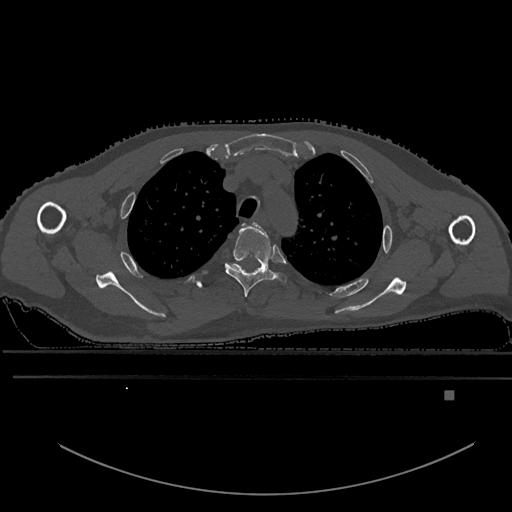
CT including the spine, one axial slice; position 449 of 969 along the scan axis; bone window (W 1800 / L 400 HU); 0.5 mm slice thickness; 512 × 512 image matrix, field of view 456 × 456 mm. Male patient, age 82 years. Case-level facts recorded for this patient, not image findings: primary cancer: prostate; vertebrae with lytic lesions (as recorded): T11, T9, T8, T2.
Outlined on this slice (semi-automatically segmented with operator editing):
- T2 vertebra: bounding box (x1, y1, x2, y2) in pixels: (242, 224, 258, 226)
- T3 vertebra: (225, 223, 287, 297)
- T4 vertebra: (227, 263, 238, 267)